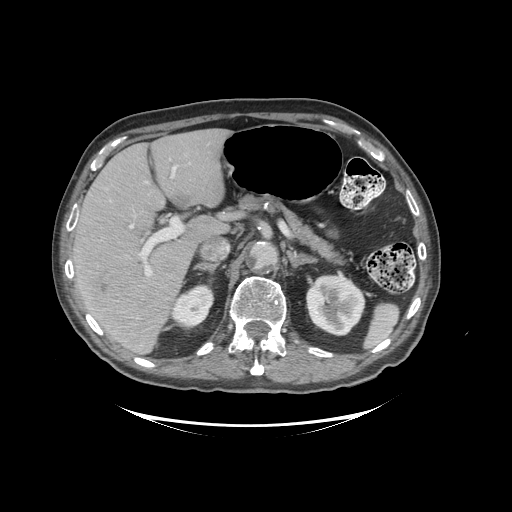
Contrast-enhanced abdominal CT (liver protocol), one axial slice; position 61 of 99 along the scan axis; soft-tissue window (W 400 / L 40 HU); 2.5 mm slice thickness; 512 × 512 image matrix, field of view 460 × 460 mm. Case-level facts recorded for this patient, not image findings: diagnosis: hepatocellular carcinoma (patient treated with transarterial chemoembolisation; whether this scan precedes or follows treatment is not stated here); TNM stage (as recorded): Stage-I; Child-Pugh class: A; tumour differentiation: moderately differentiated; tumour nodularity: uninodular.
Annotated regions visible in this slice (semi-automatic segmentation, software-assisted and operator-edited):
- liver parenchyma outside the tumour (the mass and vessels are separate outlines, so this box may not span the whole liver): bounding box [x1, y1, x2, y2] px = [72, 128, 229, 352]
- mass: [79, 263, 172, 349]
- liver vessels: [74, 166, 183, 276]